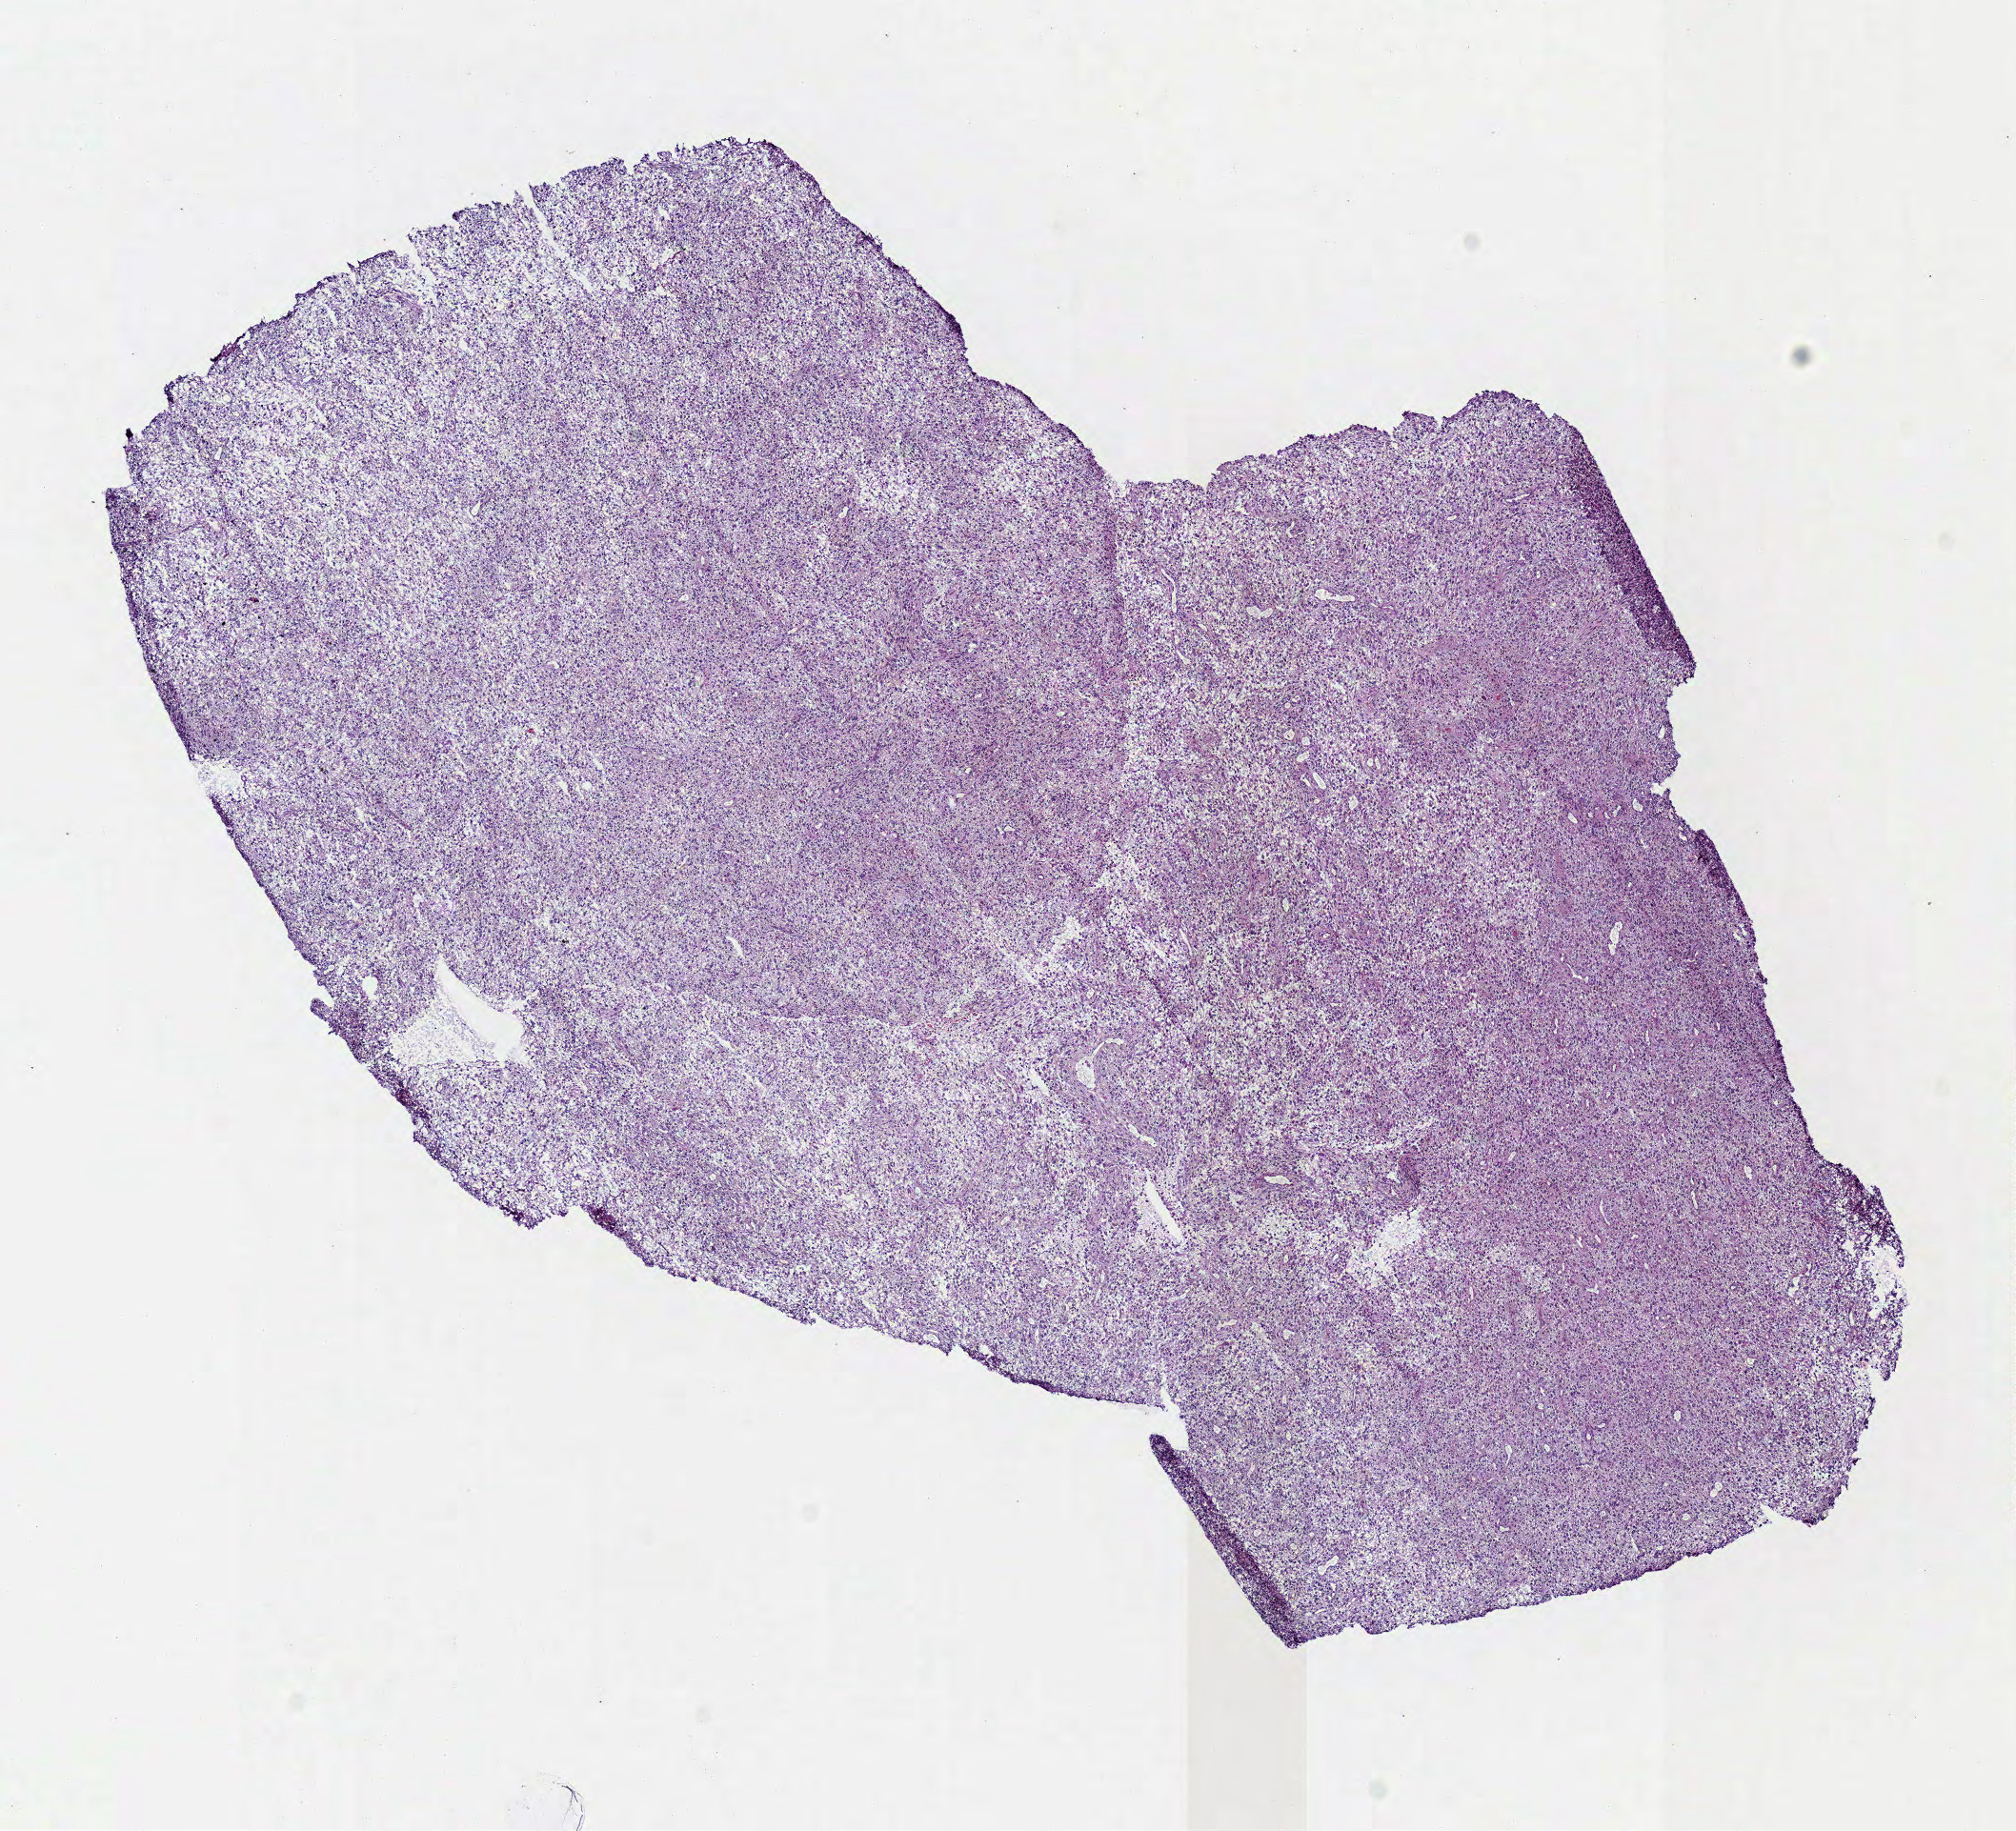
Digitized Hematoxylin and eosin (H&E) stained tissue section (whole slide) — whole scanned area (about 8.3 x 7.6 mm, slide scanned at 40x) shown as a low-resolution overview. Frozen section from the top of the tissue portion. Primary tumour sample from the brain. Female, age 60 years at initial diagnosis. Histologic grade: G3 (poorly differentiated). Slide review estimates, as recorded: tumour cells 100%, tumour nuclei 80%, normal cells 0%, stromal cells 0%, necrosis 0%.
Pathologic diagnosis: Astrocytoma, anaplastic. Laterality: left.